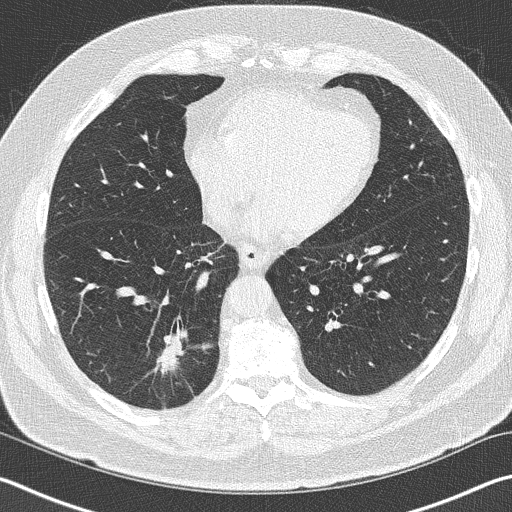
Low-dose screening chest CT, axial slice. Baseline annual screen. Lung window (W 1500 / L -600 HU). Slice 102 of 141 in the series. 512 × 512 image matrix, field of view 344 × 344 mm. Male, age 70 years at enrolment. Current smoker at enrolment.
Expert reader's lesion annotation, bounding box (x1, y1, x2, y2) in pixels: (140, 322, 211, 398). Reader record for this screening exam (exam-level; its link to the box is not recorded): non-calcified nodule or mass ≥4 mm, right lower lobe, 28 × 23 mm, spiculated (stellate) margins, soft tissue attenuation. Later outcome: lung cancer diagnosed 62 days after this screen — squamous cell carcinoma, NOS, right lower lobe, poorly differentiated (G3), stage IB (AJCC 6th edition), 24 mm at pathology.